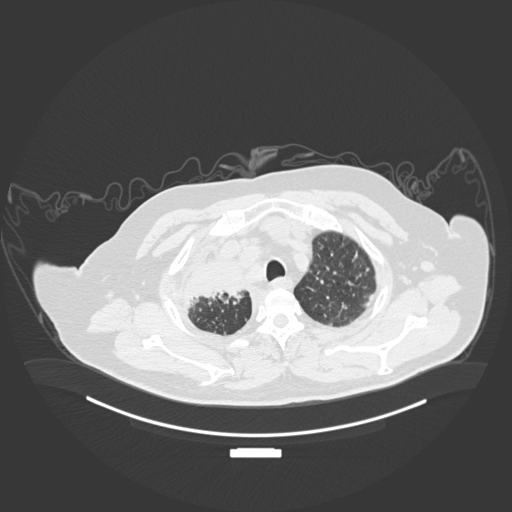
Chest CT, one axial slice. Position 160 of 201 along the scan axis. Reconstruction kernel B30f. Lung window (W 1500 / L -600 HU). 1 mm slice thickness. 512 × 512 image matrix, field of view 500 × 500 mm. Patient: male, 69 years. Case-level facts recorded for this patient, not image findings: clinical TNM (as recorded): T4 N3 M1.
Outlined on this slice (rectangle marked by the reading radiologist):
- lung tumour (recorded histology: adenocarcinoma): bounding box <167,251,247,307> (left, top, right, bottom; pixels)